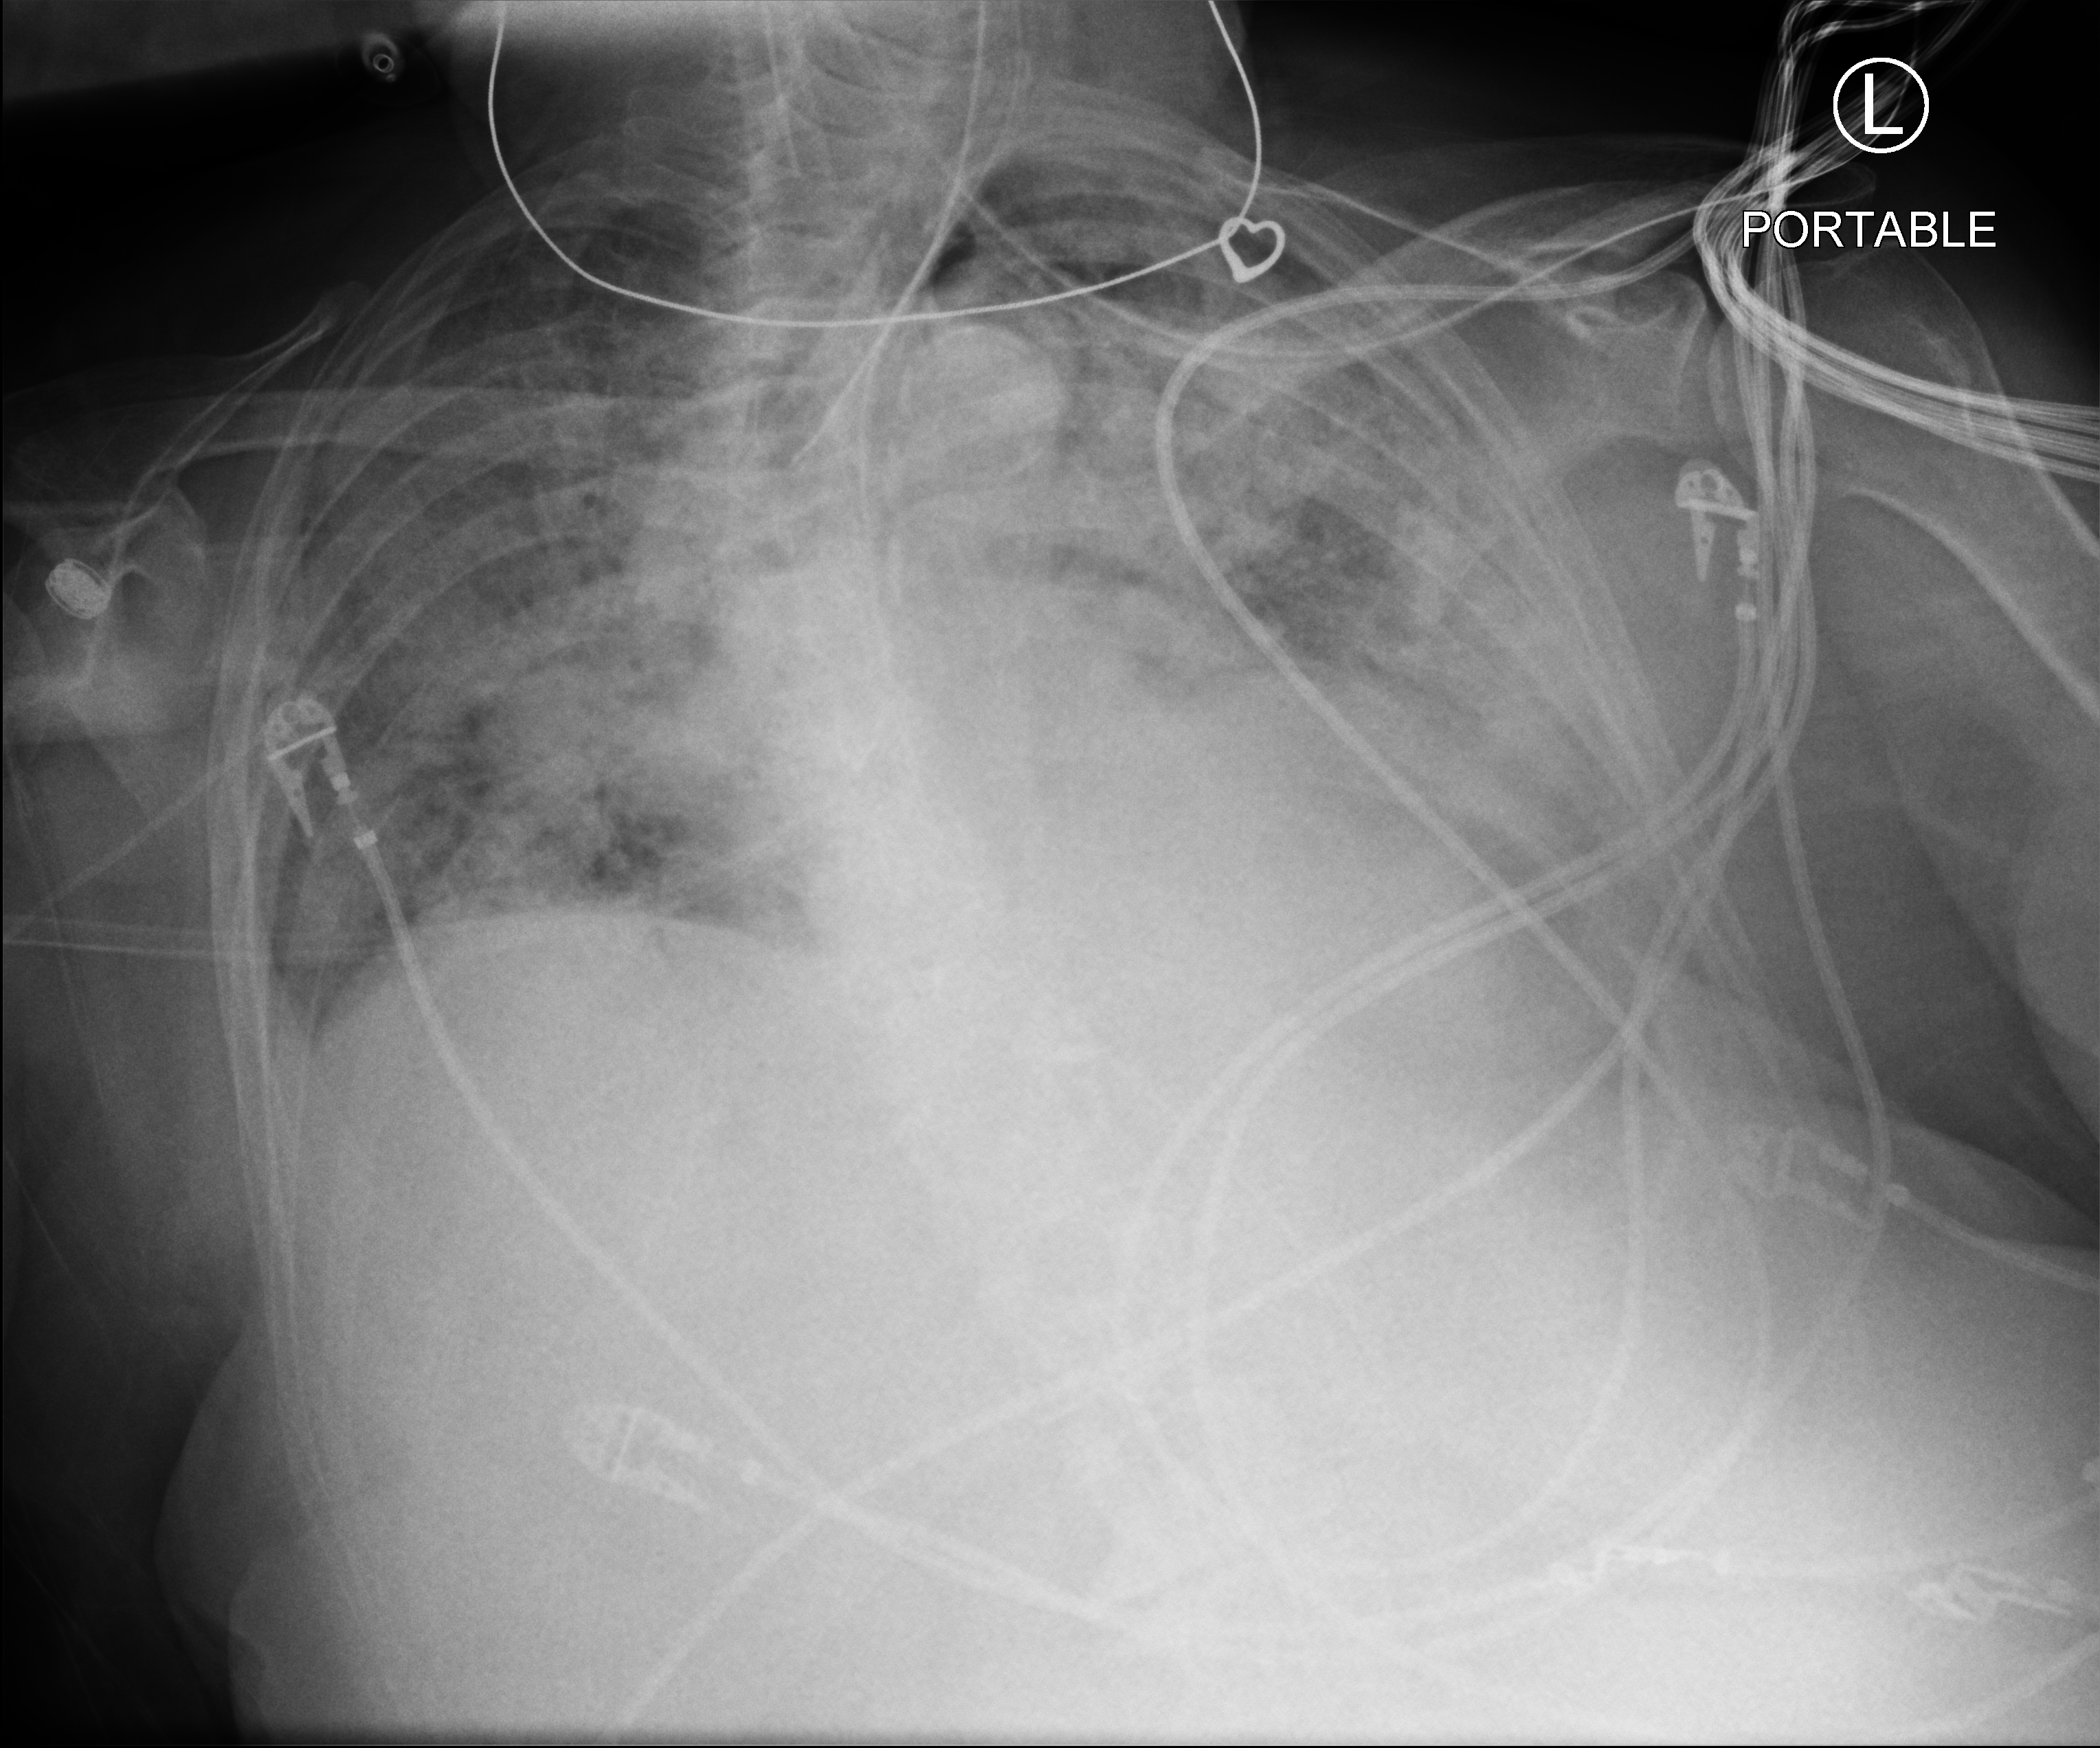
Chest X-ray (portable), anteroposterior (AP) projection. Patient hospitalised with COVID-19; female, aged 75–90 years.
Admission-level facts for this patient (not findings on this image; timing relative to this image not recorded):
- mechanically ventilated during this hospital stay: yes
- admitted to intensive care during this hospital stay: yes
- diabetes (admission record): no